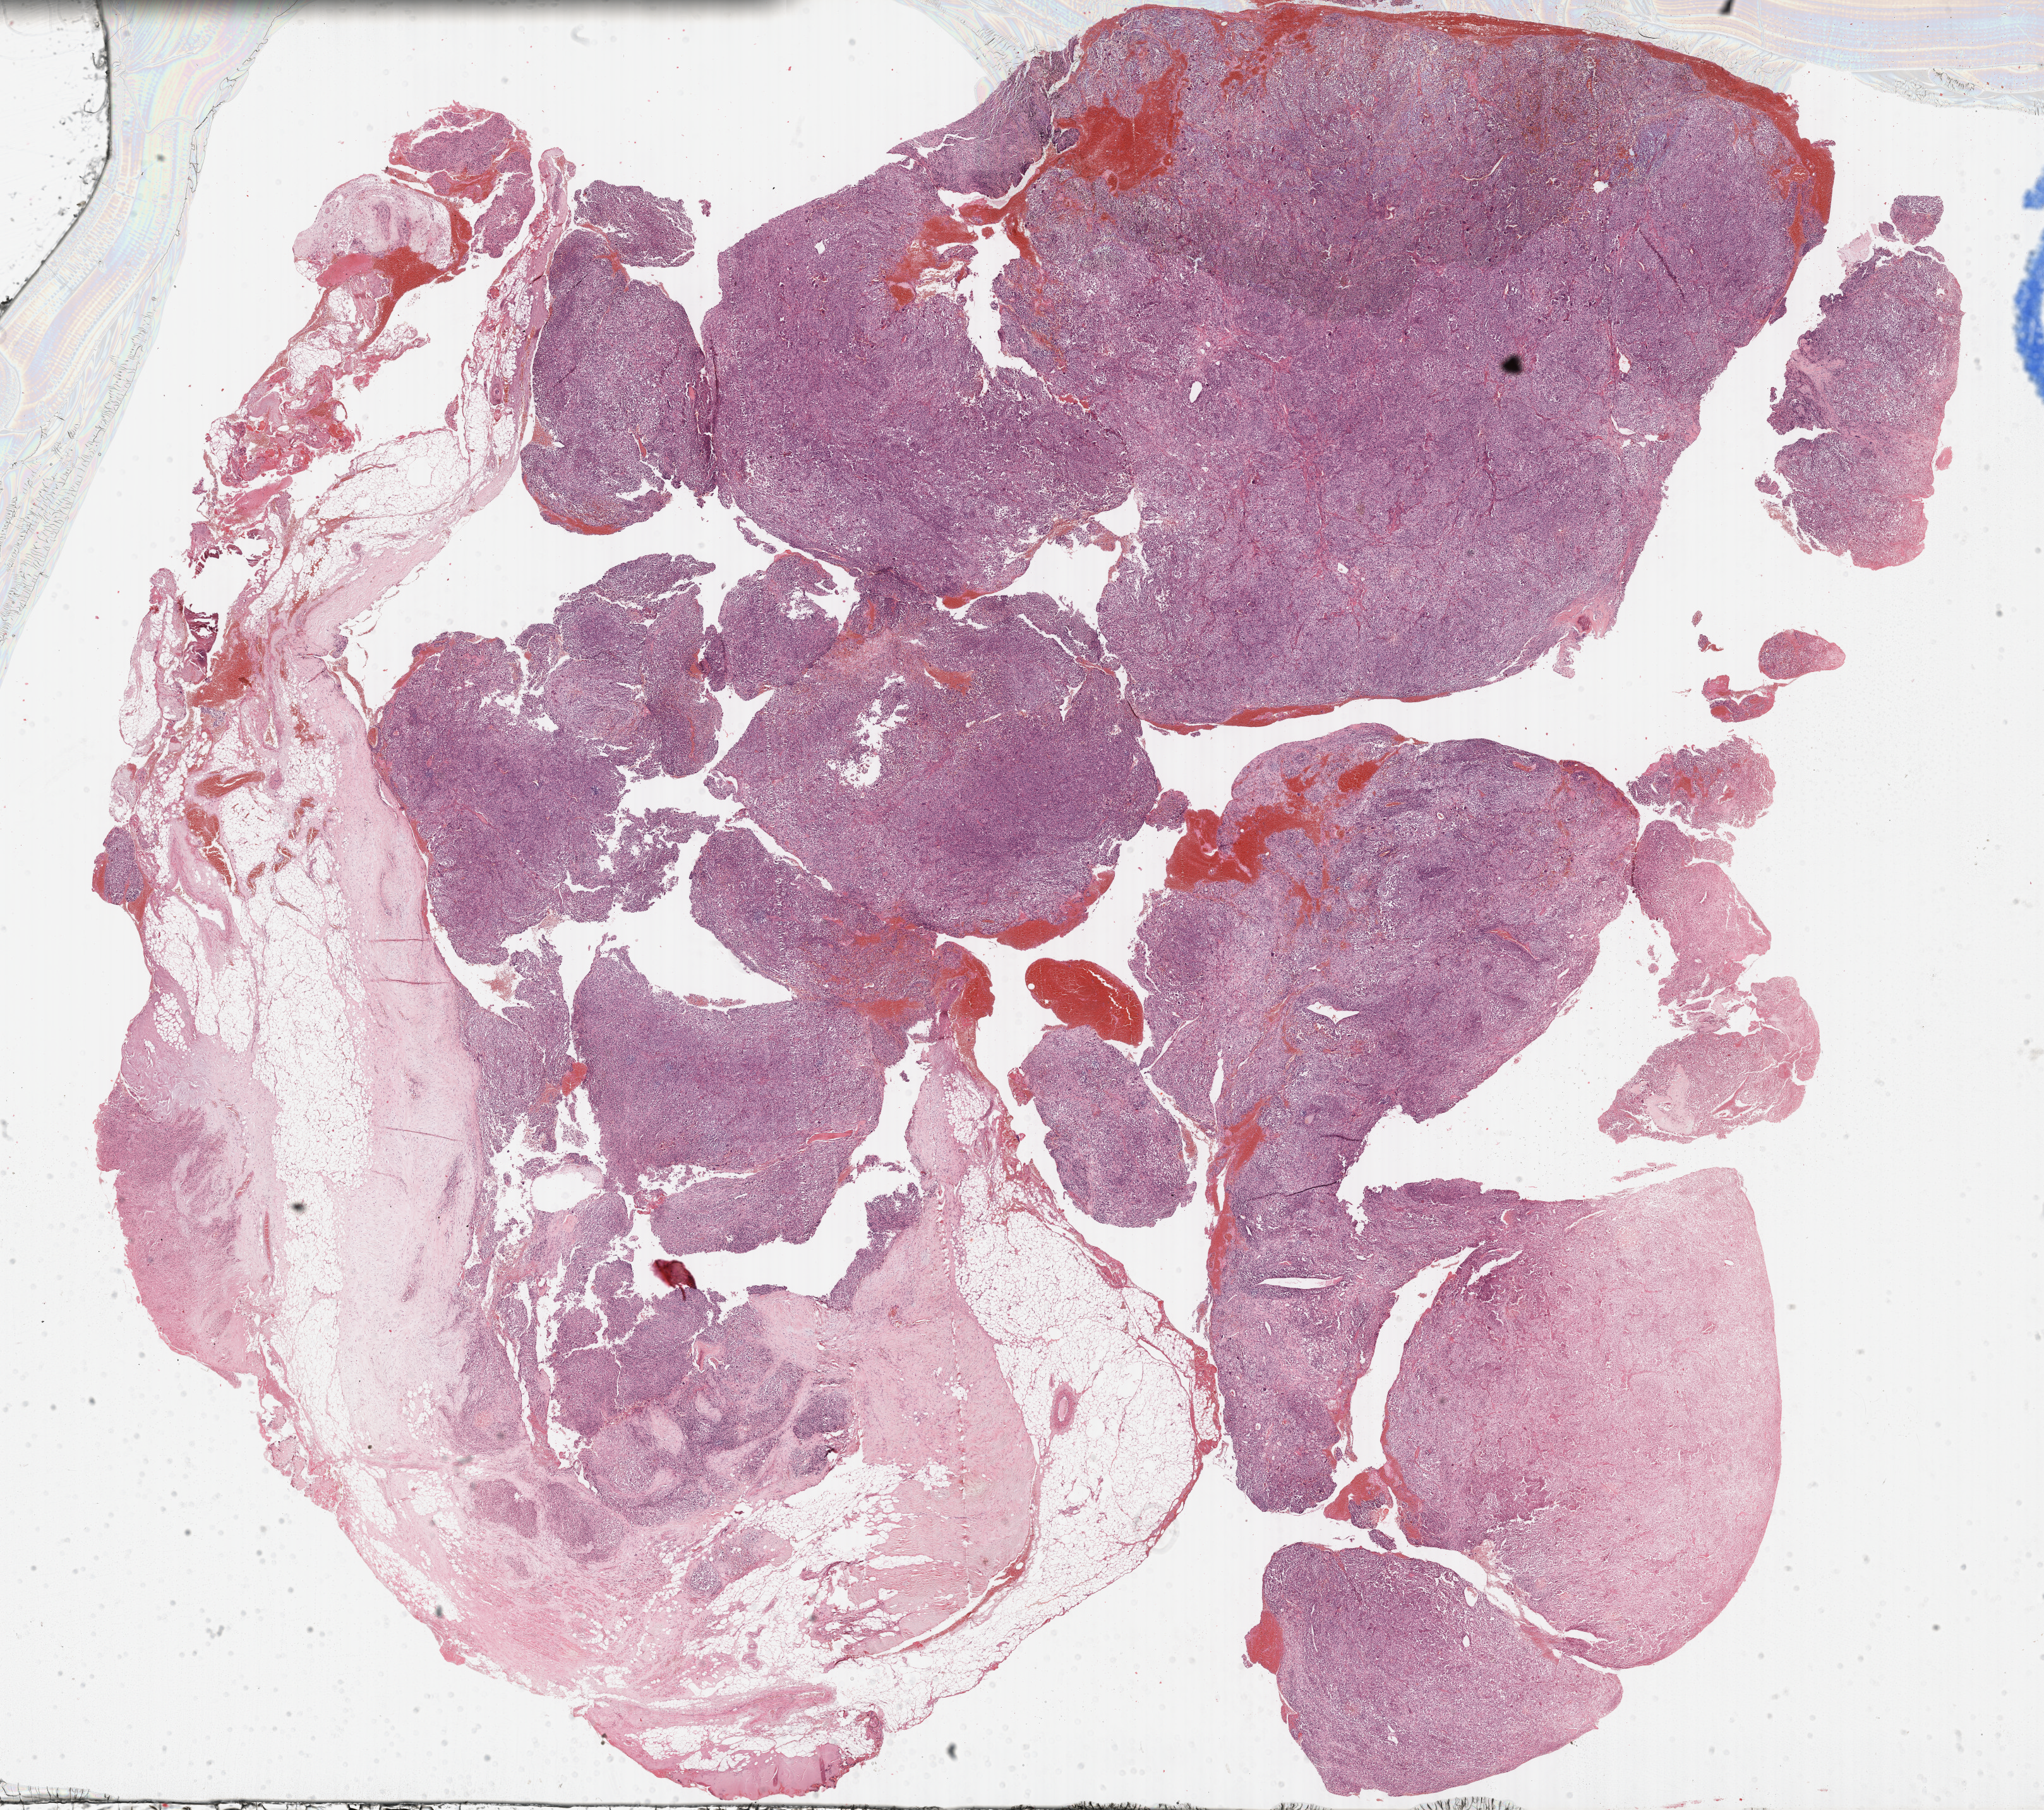
H&E-stained whole-slide image, low-resolution overview of the scanned area, about 26.2 x 23.2 mm (acquisition: 40x scan), formalin-fixed paraffin-embedded (FFPE) diagnostic section, primary tumour sample from the adrenal cortex. Female patient; age at initial diagnosis 44 years.
Lymph nodes positive (case pathology): 0 of 1 examined. Pathologic diagnosis: Adrenal cortical carcinoma (cortex of adrenal gland).